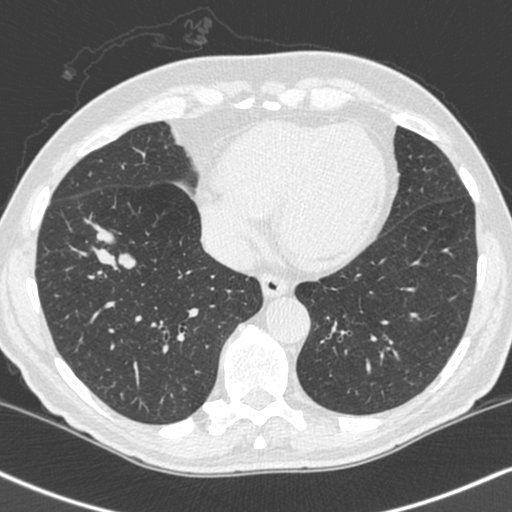
Chest CT (low-dose screening protocol), one axial image; baseline screening round; lung window (W 1500 / L -600 HU); 1.3 mm slice thickness; standard (soft-tissue) reconstruction kernel (C); 120 kVp; 512 × 512 image matrix. Male participant, aged 68 years at enrolment. Current smoker at enrolment.
- Expert-annotated lung lesion, bounding box [x1, y1, x2, y2] px = [77, 202, 152, 271].
- The exam's reader record, not a measurement of the box and not confirmed to be the same lesion: non-calcified nodule or mass ≥4 mm, right lower lobe, 34 × 17 mm, smooth margins, soft tissue attenuation.
- Later outcome: lung cancer diagnosed 24 days after this screen — combined small cell carcinoma, right lower lobe, stage IIIA (AJCC 6th edition), 41 mm at pathology.